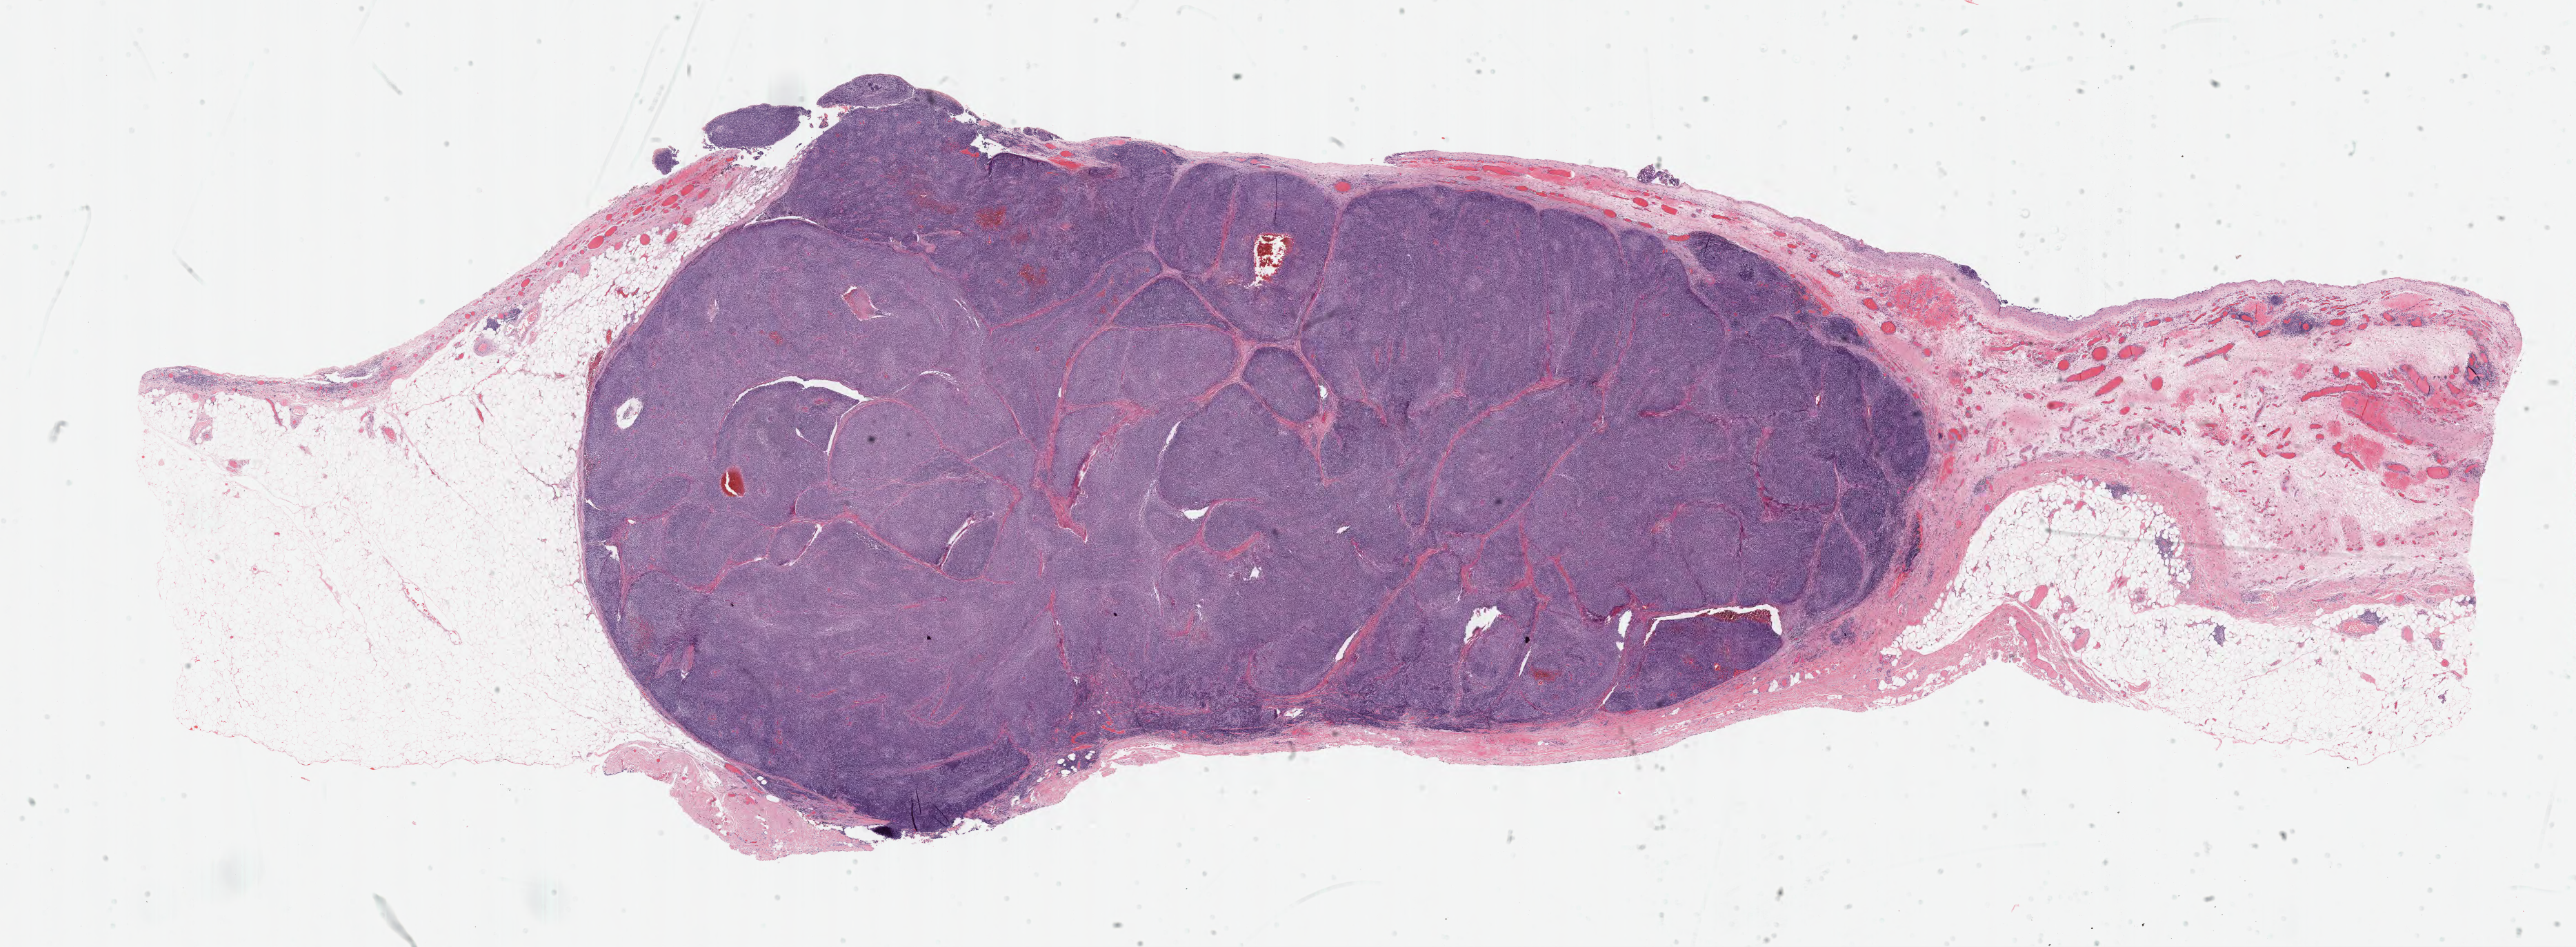
Whole-slide histology image, Hematoxylin and eosin (H&E) stained — shown as a low-resolution overview of the whole scanned area (about 30.2 x 11.1 mm), FFPE section, sample: primary tumour, thymus. Patient: male, age at initial diagnosis 45 years.
Histologic diagnosis: Thymoma, type B1, malignant.